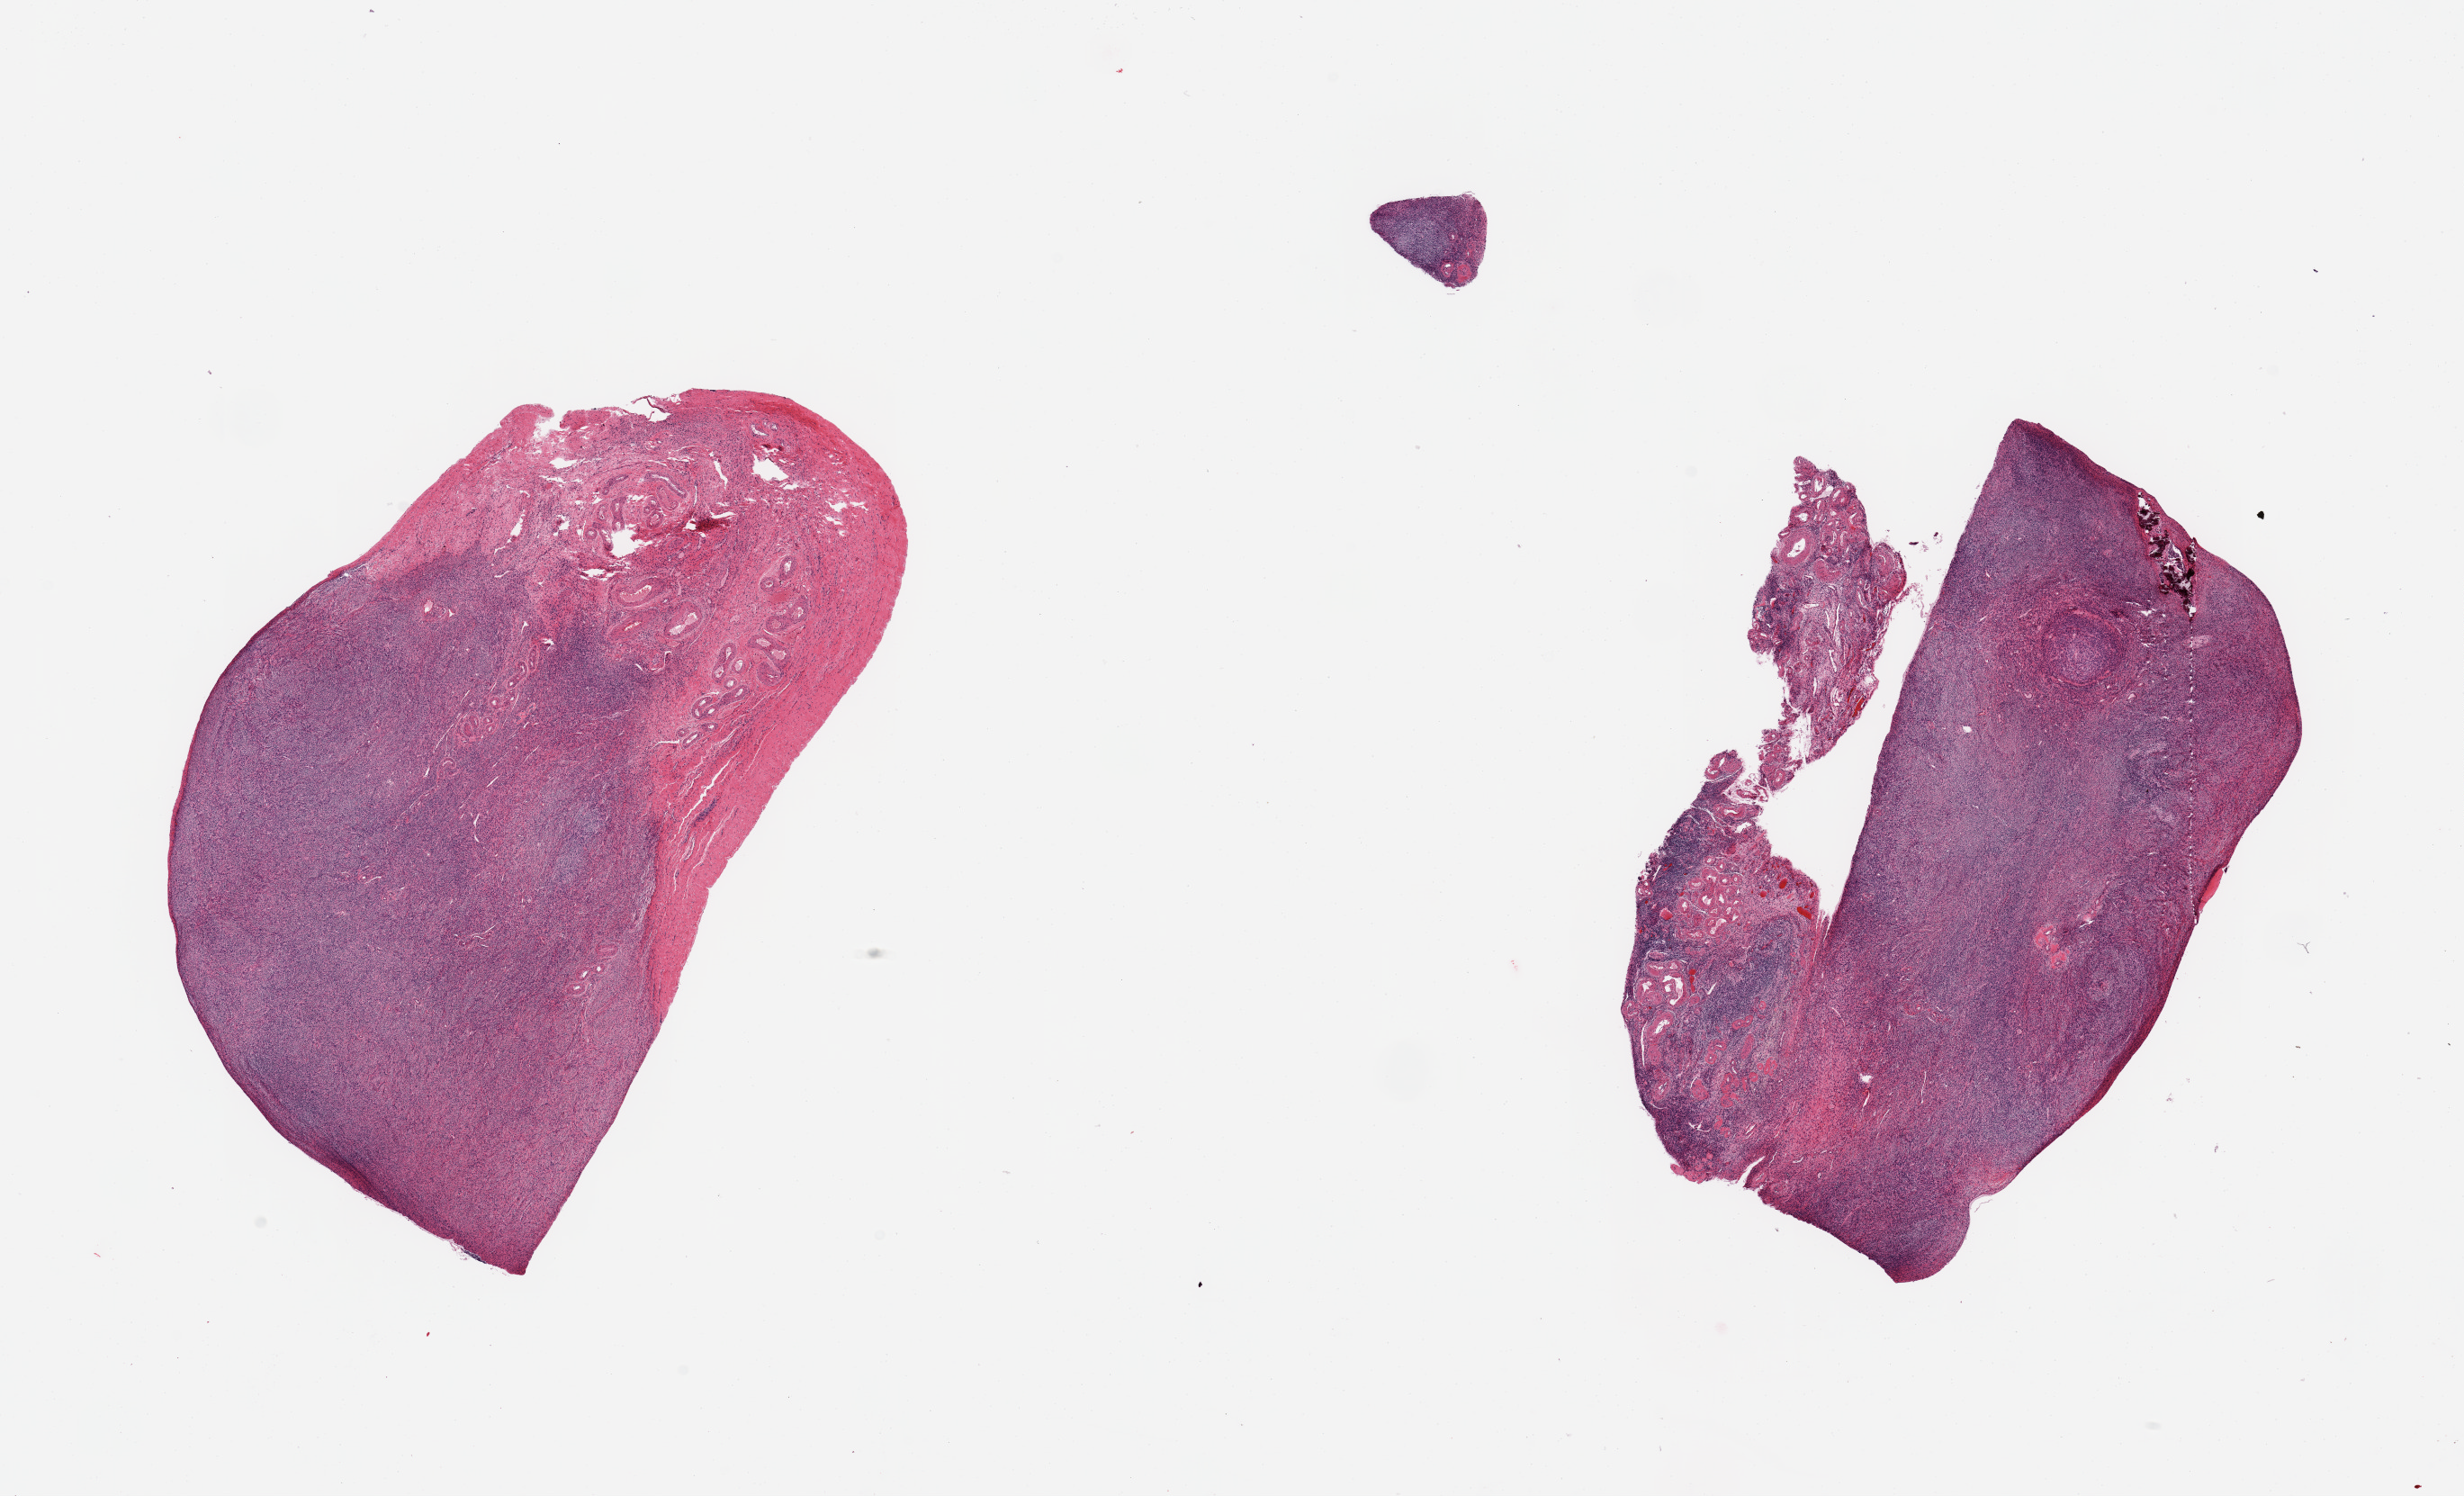
Digitized hematoxylin and eosin (H&E)-stained section, low-resolution overview of the scanned area, about 21.7 x 13.1 mm (slide scanned at 20x), PAXgene-fixed, paraffin-embedded tissue, target tissue: ovary, donor tissue sample.
* review note (as recorded): 2 pieces, stroma, no abnormality, post menopausal atrophy